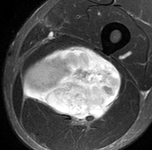
MRI of an extremity soft-tissue mass, one axial slice. Slice 59 of 90 in the series (ordered by position). STIR. MR volume resampled by the dataset authors to the PET/CT grid (not the native acquisition matrix). 3.27 mm slice thickness. 152 × 150 image matrix, field of view 148 × 146 mm. Male patient. Case-level facts recorded for this patient, not image findings: histological type: undifferentiated pleomorphic liposarcoma; grade: high; site of the primary tumour: left thigh.
Outlined on this slice (expert contour drawn on MRI and transferred to this co-registered scan by the dataset authors):
- gross tumour volume including surrounding oedema: bounding box [x1, y1, x2, y2] px = [20, 44, 122, 127]
- gross tumour volume (mass): [20, 44, 122, 124]